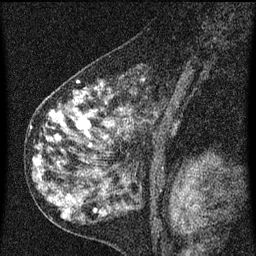
Breast MRI (dynamic contrast-enhanced), one sagittal slice; dynamic contrast-enhanced series, image 2 of 3 at this slice position (ordered by acquisition); 1.5 T; TE 4.2 ms, TR 8 ms; 2 mm slice thickness; 256 × 256 image matrix, field of view 180 × 180 mm. Patient: female, 55 years.
Annotated regions visible in this slice (semi-automatically segmented with operator editing):
- analysis volume of interest (the breast-tissue region the enhancement analysis was run in; not a lesion): box from (x=42, y=72) to (x=185, y=155) px
- tumour enhancement mask (voxels above the 70 % enhancement threshold inside the analysis volume of interest): (x=50, y=82)–(x=123, y=147)